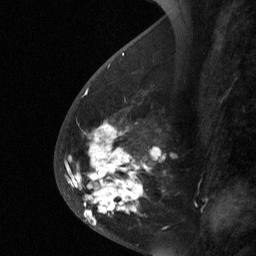
Breast MRI (dynamic contrast-enhanced), one sagittal slice. Slice 24 of 64 in the series (ordered by position). Dynamic contrast-enhanced study with each time point stored as its own series, time point 2 of 3 at this slice position (early post-contrast, ordered by acquisition time). 1.5 T. TE 4.8 ms, TR 27 ms. 2 mm slice thickness. 256 × 256 image matrix, field of view 180 × 180 mm. Female patient, age 56 years. Case-level facts recorded for this patient, not image findings: setting: breast cancer imaged before/during neoadjuvant chemotherapy; receptor status: HER2-positive.
Outlined on this slice (semi-automatically segmented with operator editing):
- analysis volume of interest (the breast-tissue region the enhancement analysis was run in; not a lesion): bounding box (x1, y1, x2, y2) in pixels: (59, 104, 169, 229)
- tumour enhancement mask (voxels above the 90 % enhancement threshold inside the analysis volume of interest): (66, 125, 157, 225)